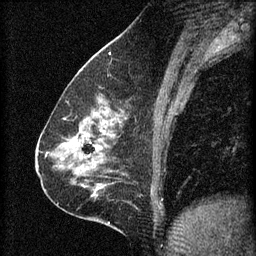
Breast MRI (dynamic contrast-enhanced), one sagittal slice; position 30 of 60 along the scan axis; 3 images stored at this slice position (order not interpretable as contrast timing); 1.5 T; TE 4.2 ms, TR 8.2 ms; 2 mm slice thickness; 256 × 256 image matrix, field of view 180 × 180 mm. Patient: female, 59 years.
Outlined on this slice (semi-automatic segmentation, software-assisted and operator-edited):
- analysis volume of interest (the breast-tissue region the enhancement analysis was run in; not a lesion): box from (x=61, y=104) to (x=130, y=161) px
- tumour enhancement mask (voxels above the 70 % enhancement threshold inside the analysis volume of interest): (x=65, y=110)–(x=120, y=157)